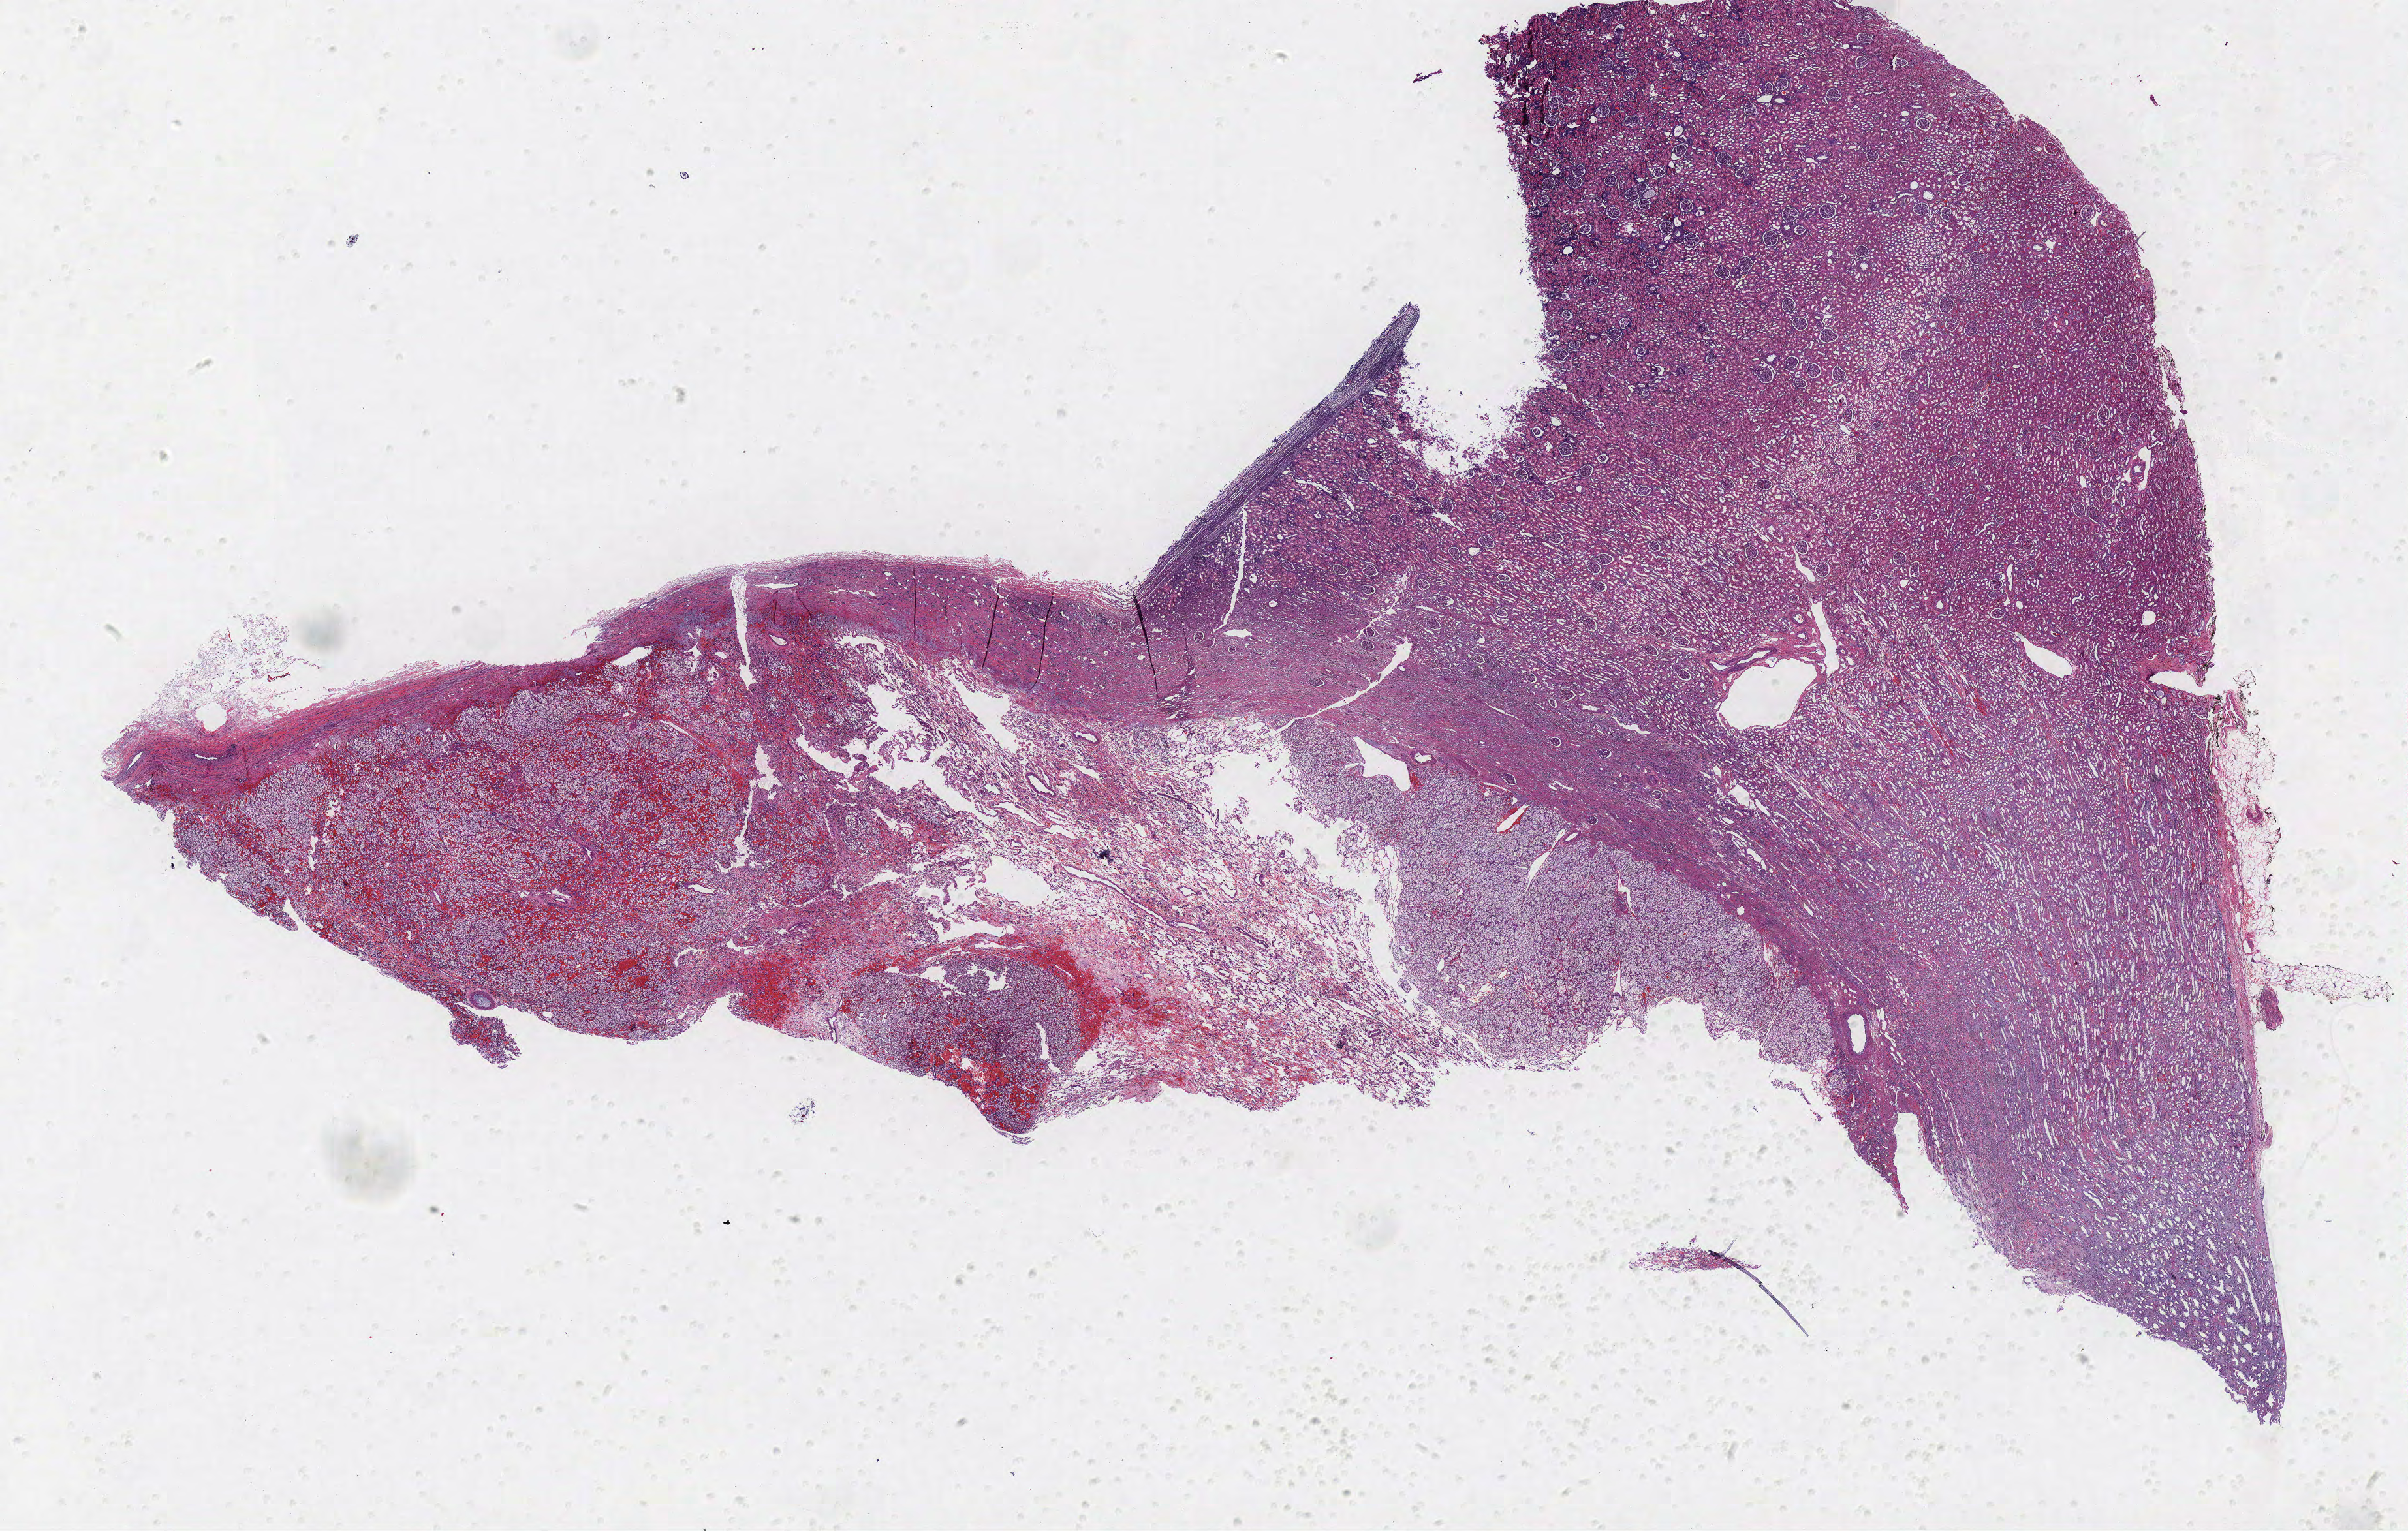
Digitized H&E-stained tissue section (whole slide), shown as a low-resolution overview of the whole scanned area (about 29.5 x 18.8 mm, from a 40x scan), FFPE section, sample: primary tumour, kidney. Male, age 43 years at initial diagnosis. Histologic grade: G2 (moderately differentiated).
Histologic diagnosis: Clear cell adenocarcinoma, NOS. TNM: T1a NX M0. AJCC pathologic stage: I.